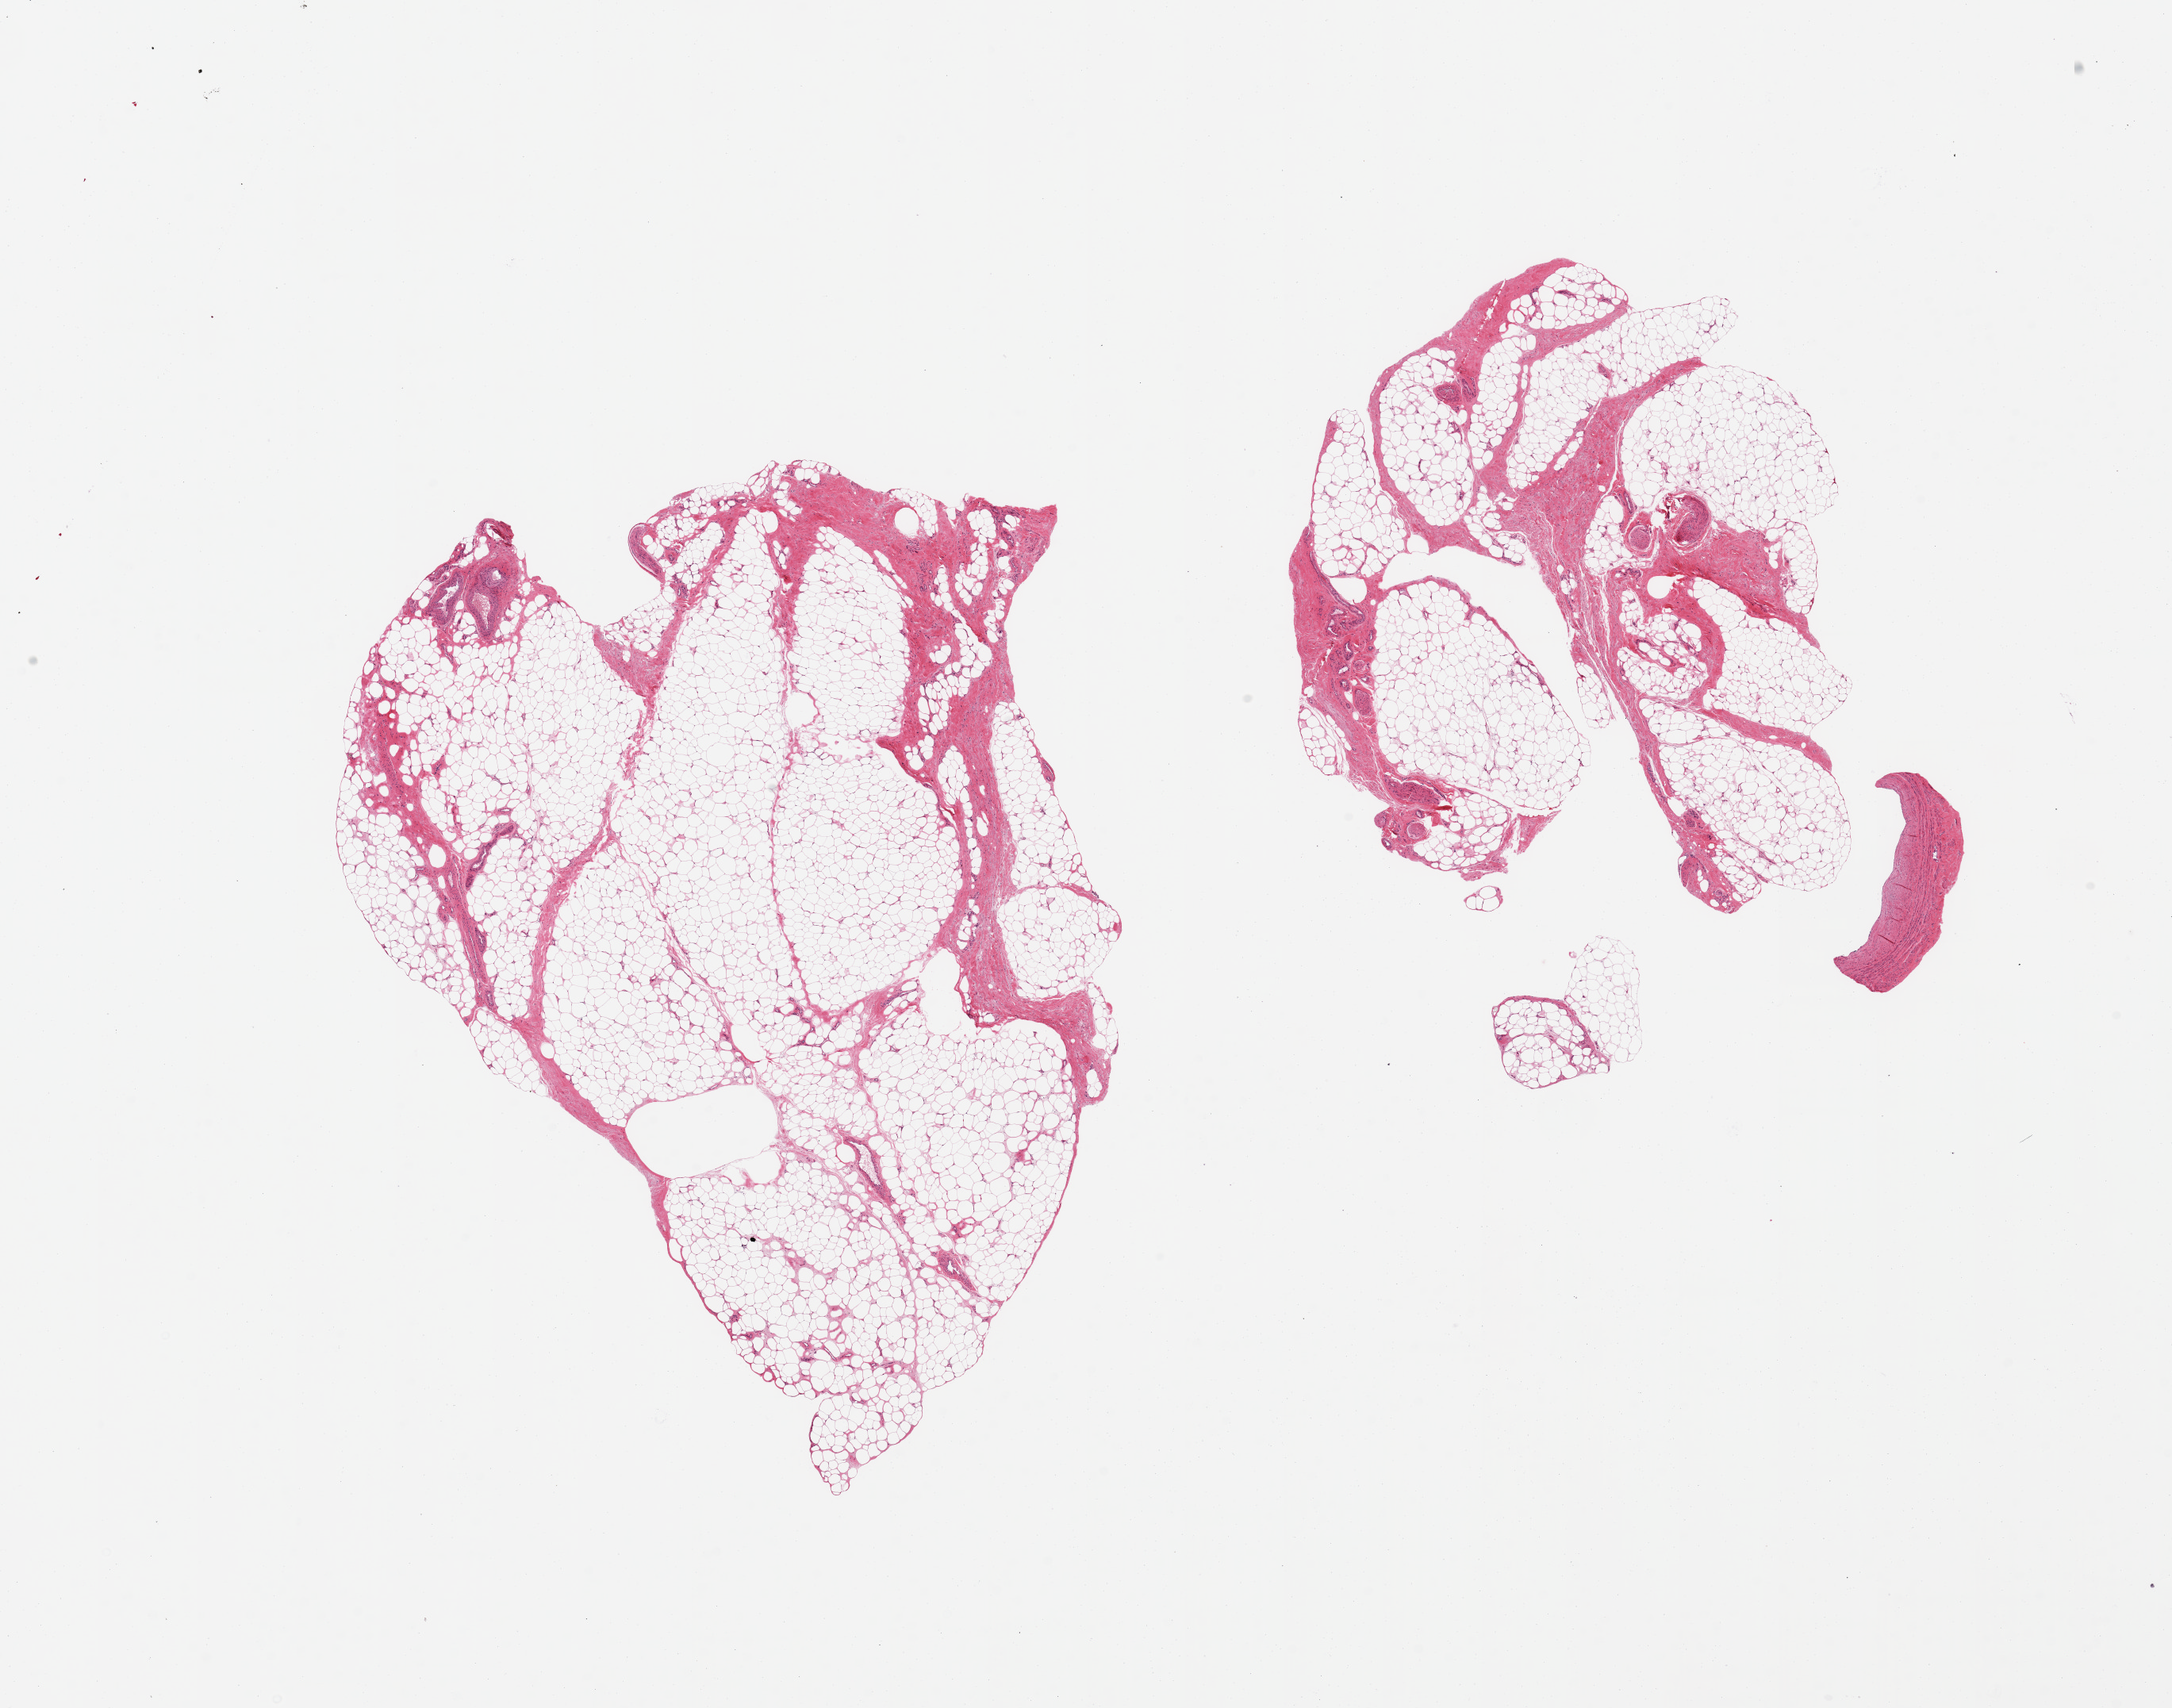
H&E whole-slide image, brightfield, shown as a low-resolution overview of the whole scanned area (about 21.7 x 17.0 mm, from a 20x scan). PAXgene-fixed paraffin-embedded (PFPE) section. Section of adipose tissue (target tissue). Donor tissue sample.
Review note (as recorded): 2 pieces, ~25% fascia/vascular elements.